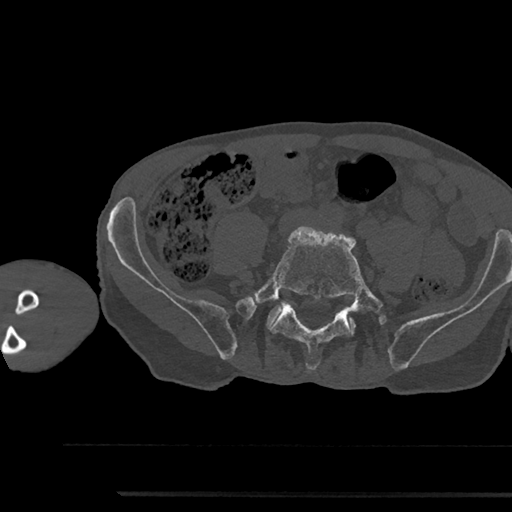
CT including the spine, one axial slice. Position 343 of 797 along the scan axis. Bone window (W 1800 / L 400 HU). 512 × 512 image matrix, field of view 367 × 367 mm. Male patient, age 79 years. Case-level facts recorded for this patient, not image findings: primary cancer: prostate.
Outlined on this slice (semi-automatic segmentation, software-assisted and operator-edited):
- L5 vertebra: box from (x=253, y=226) to (x=383, y=370) px